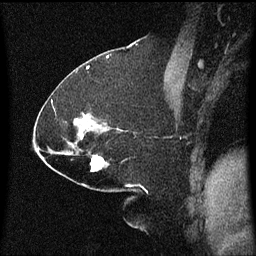
Breast MRI (dynamic contrast-enhanced), one sagittal slice; slice 32 of 60 in the series (ordered by position); dynamic contrast-enhanced series, image 2 of 3 at this slice position (ordered by acquisition); 1.5 T; TE 4.2 ms, TR 8 ms; 2.1 mm slice thickness; 256 × 256 image matrix, field of view 200 × 200 mm. Patient: female, 59 years.
Structures marked on this image (semi-automatically segmented with operator editing):
- analysis volume of interest (the breast-tissue region the enhancement analysis was run in; not a lesion): box from (x=90, y=152) to (x=109, y=173) px
- tumour enhancement mask (voxels above the 70 % enhancement threshold inside the analysis volume of interest): (x=90, y=156)–(x=105, y=171)